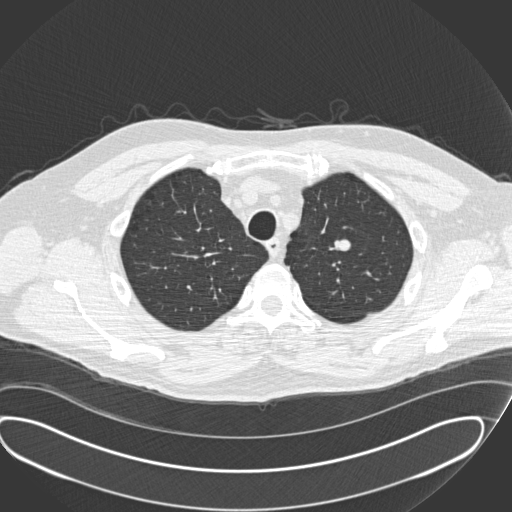
Axial slice from a low-dose chest CT screening exam. Second annual screen. Lung window (W 1500 / L -600 HU). 2 mm slice thickness. Male, age 56 years at enrolment. Current smoker at enrolment.
Lesion marked by an expert reader, bounding box [x1, y1, x2, y2] px = [313, 227, 369, 271]. No non-calcified nodule or mass ≥4 mm was recorded by the screening reader at this exam. Lung cancer was diagnosed 520 days after this screen (after the third annual screen): neuroendocrine carcinoma, NOS, left upper lobe, well differentiated (G1), stage IA (AJCC 6th edition), 20 mm at pathology.